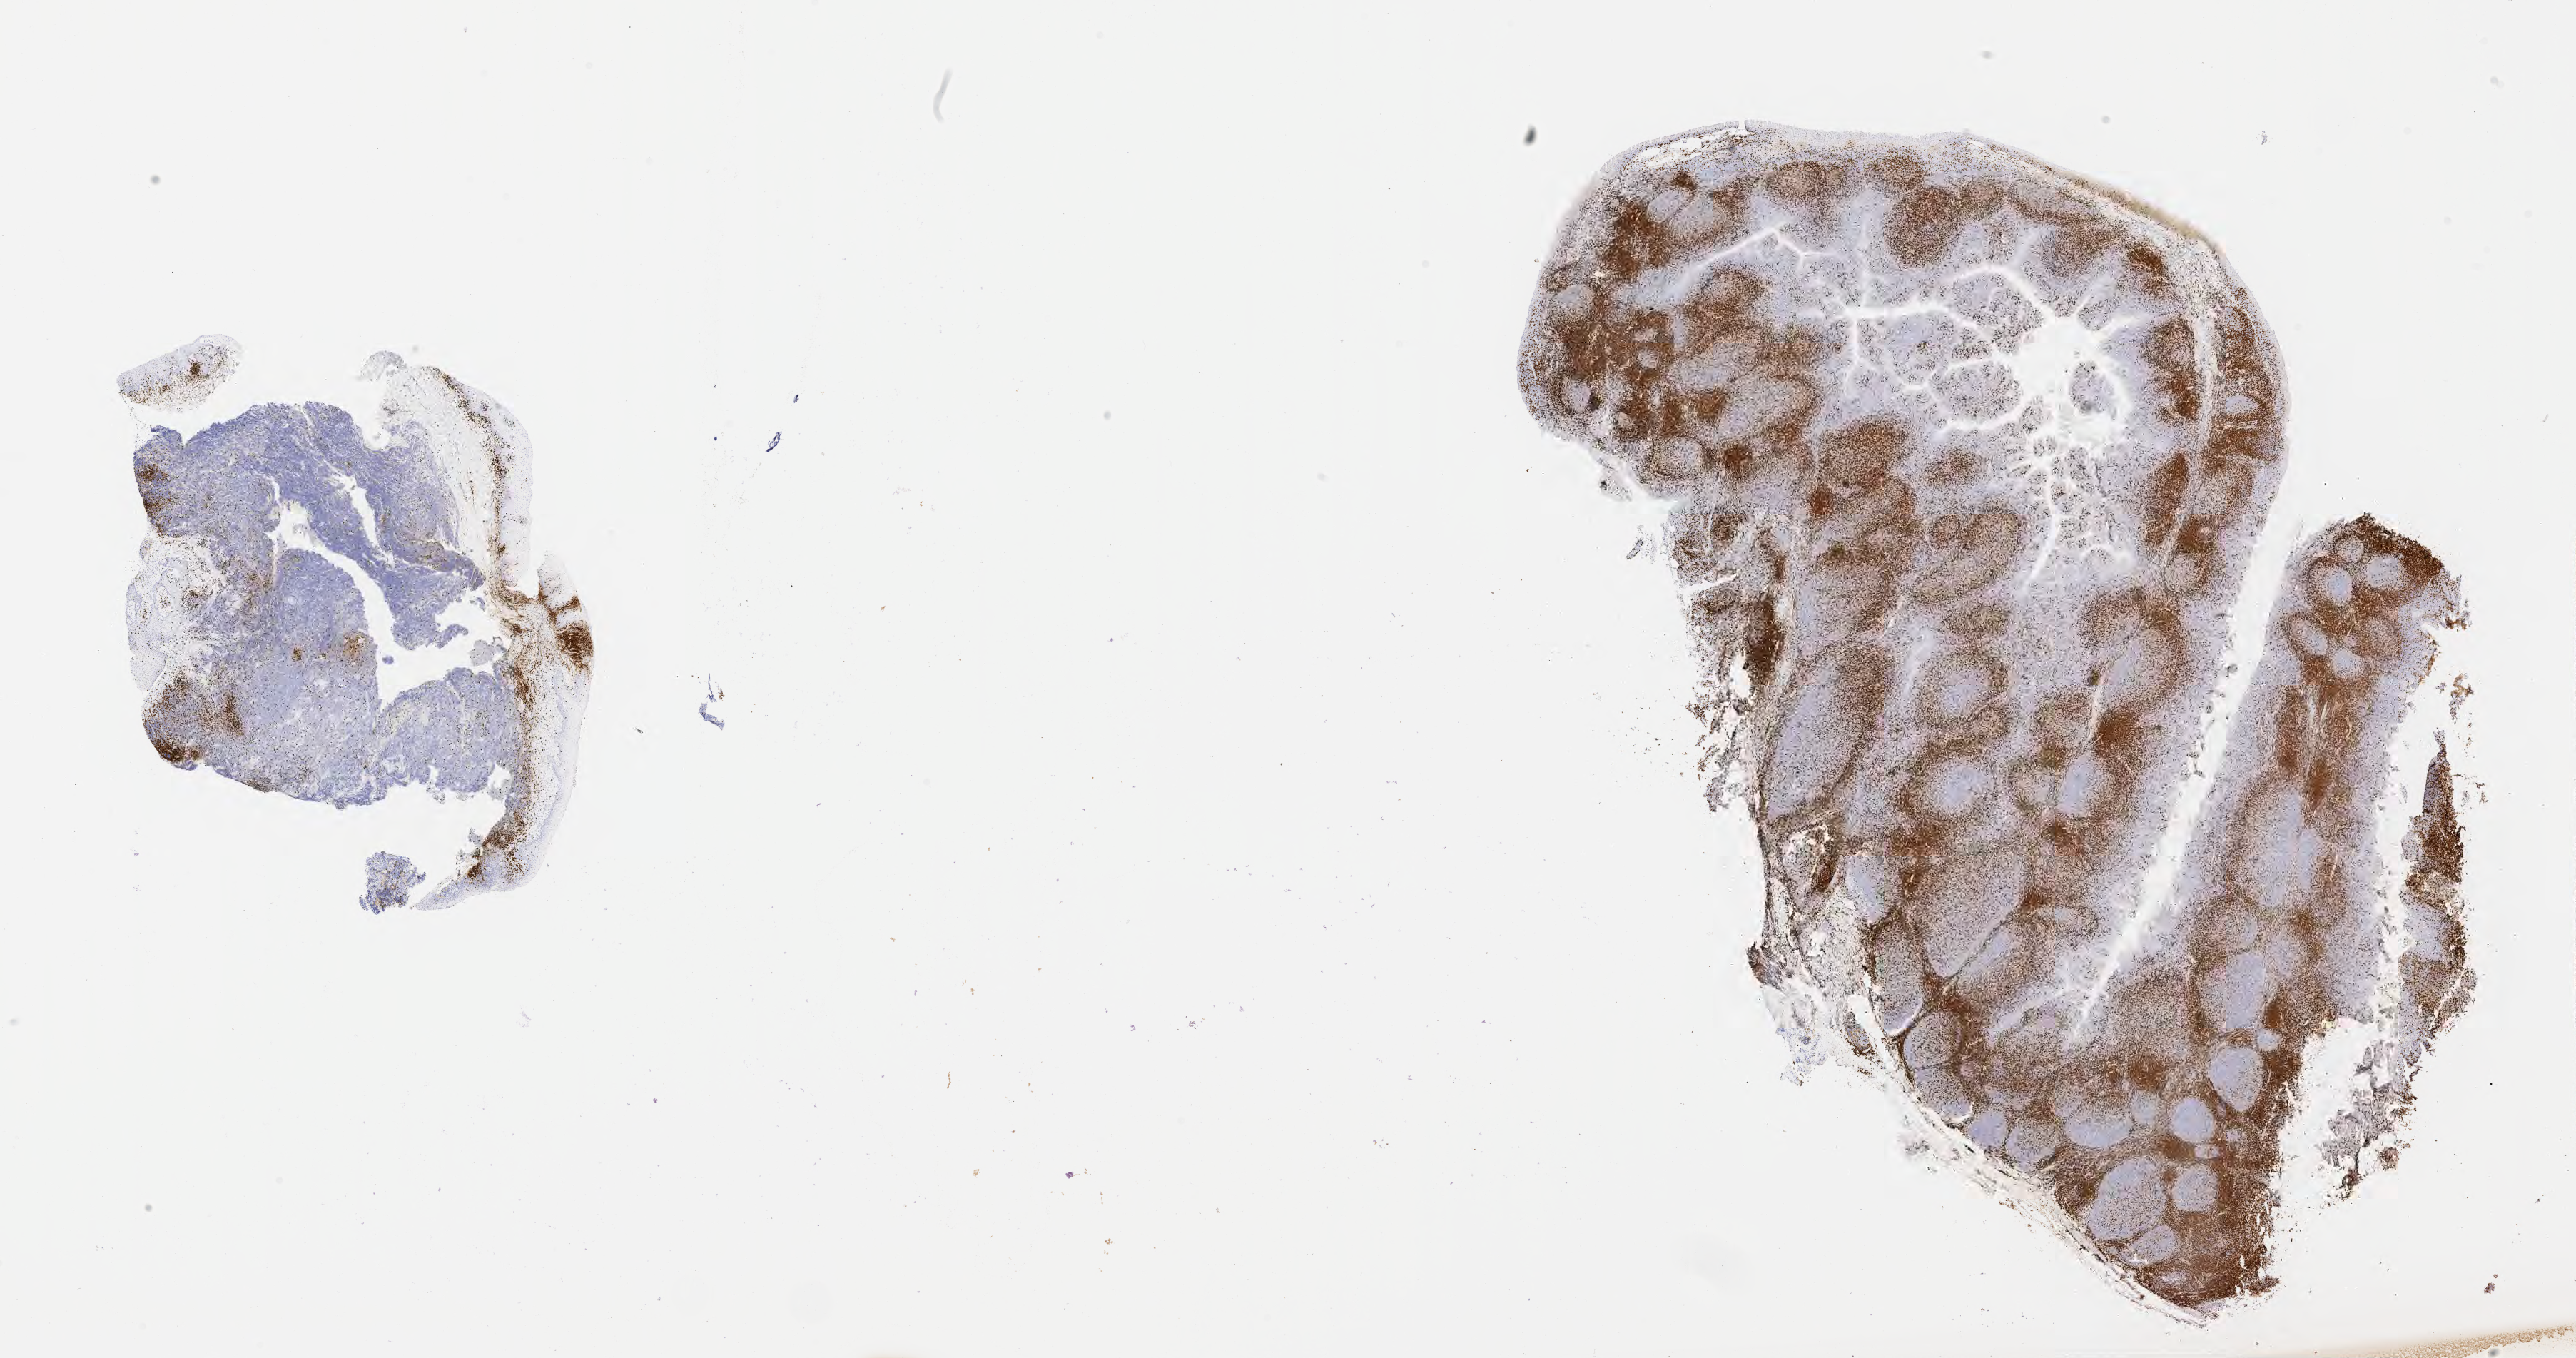
IHC for CD3, whole-slide image — low-resolution overview of the scanned area, about 29.2 x 15.4 mm; tumor tissue; anatomic site: mandible. Female patient; age at initial diagnosis 7 years.
Diagnosis: Burkitt lymphoma, NOS.